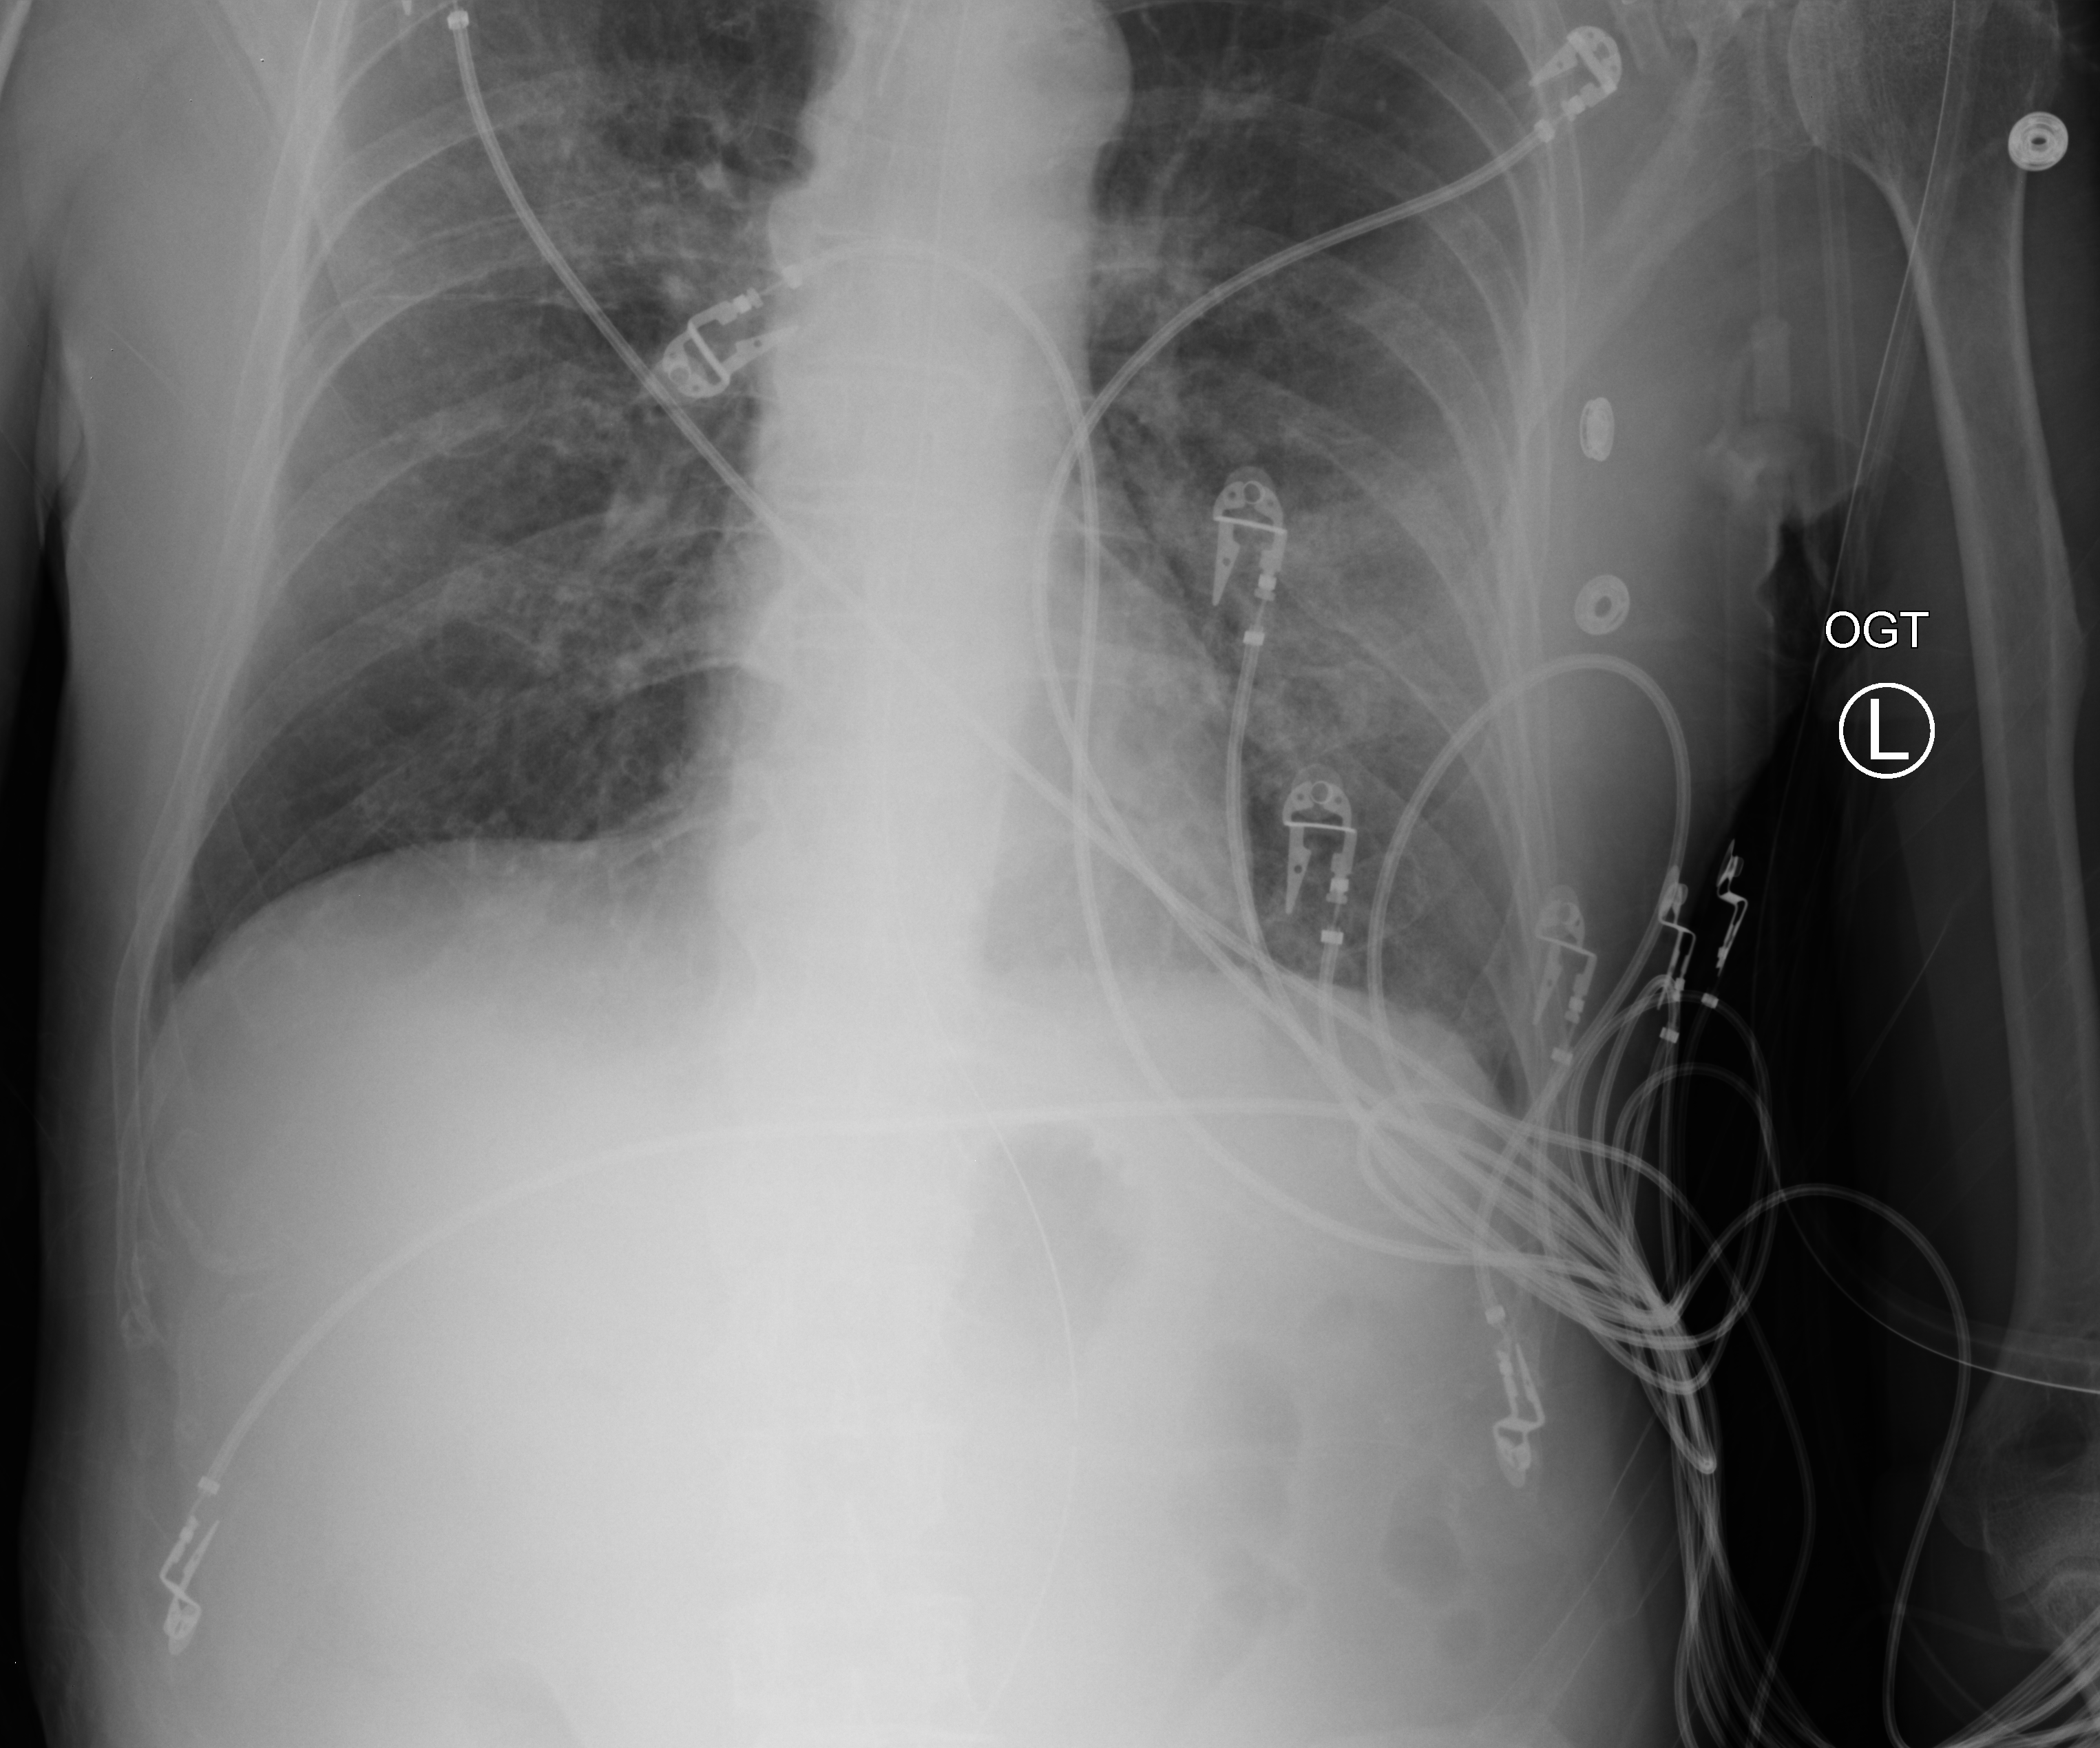
Chest X-ray (portable). Patient hospitalised with COVID-19; male, aged 60–74 years.
Hospital-stay facts (about this admission, not read from this image; timing relative to this image not recorded):
- mechanically ventilated during this hospital stay: yes
- smoking status (admission record): current